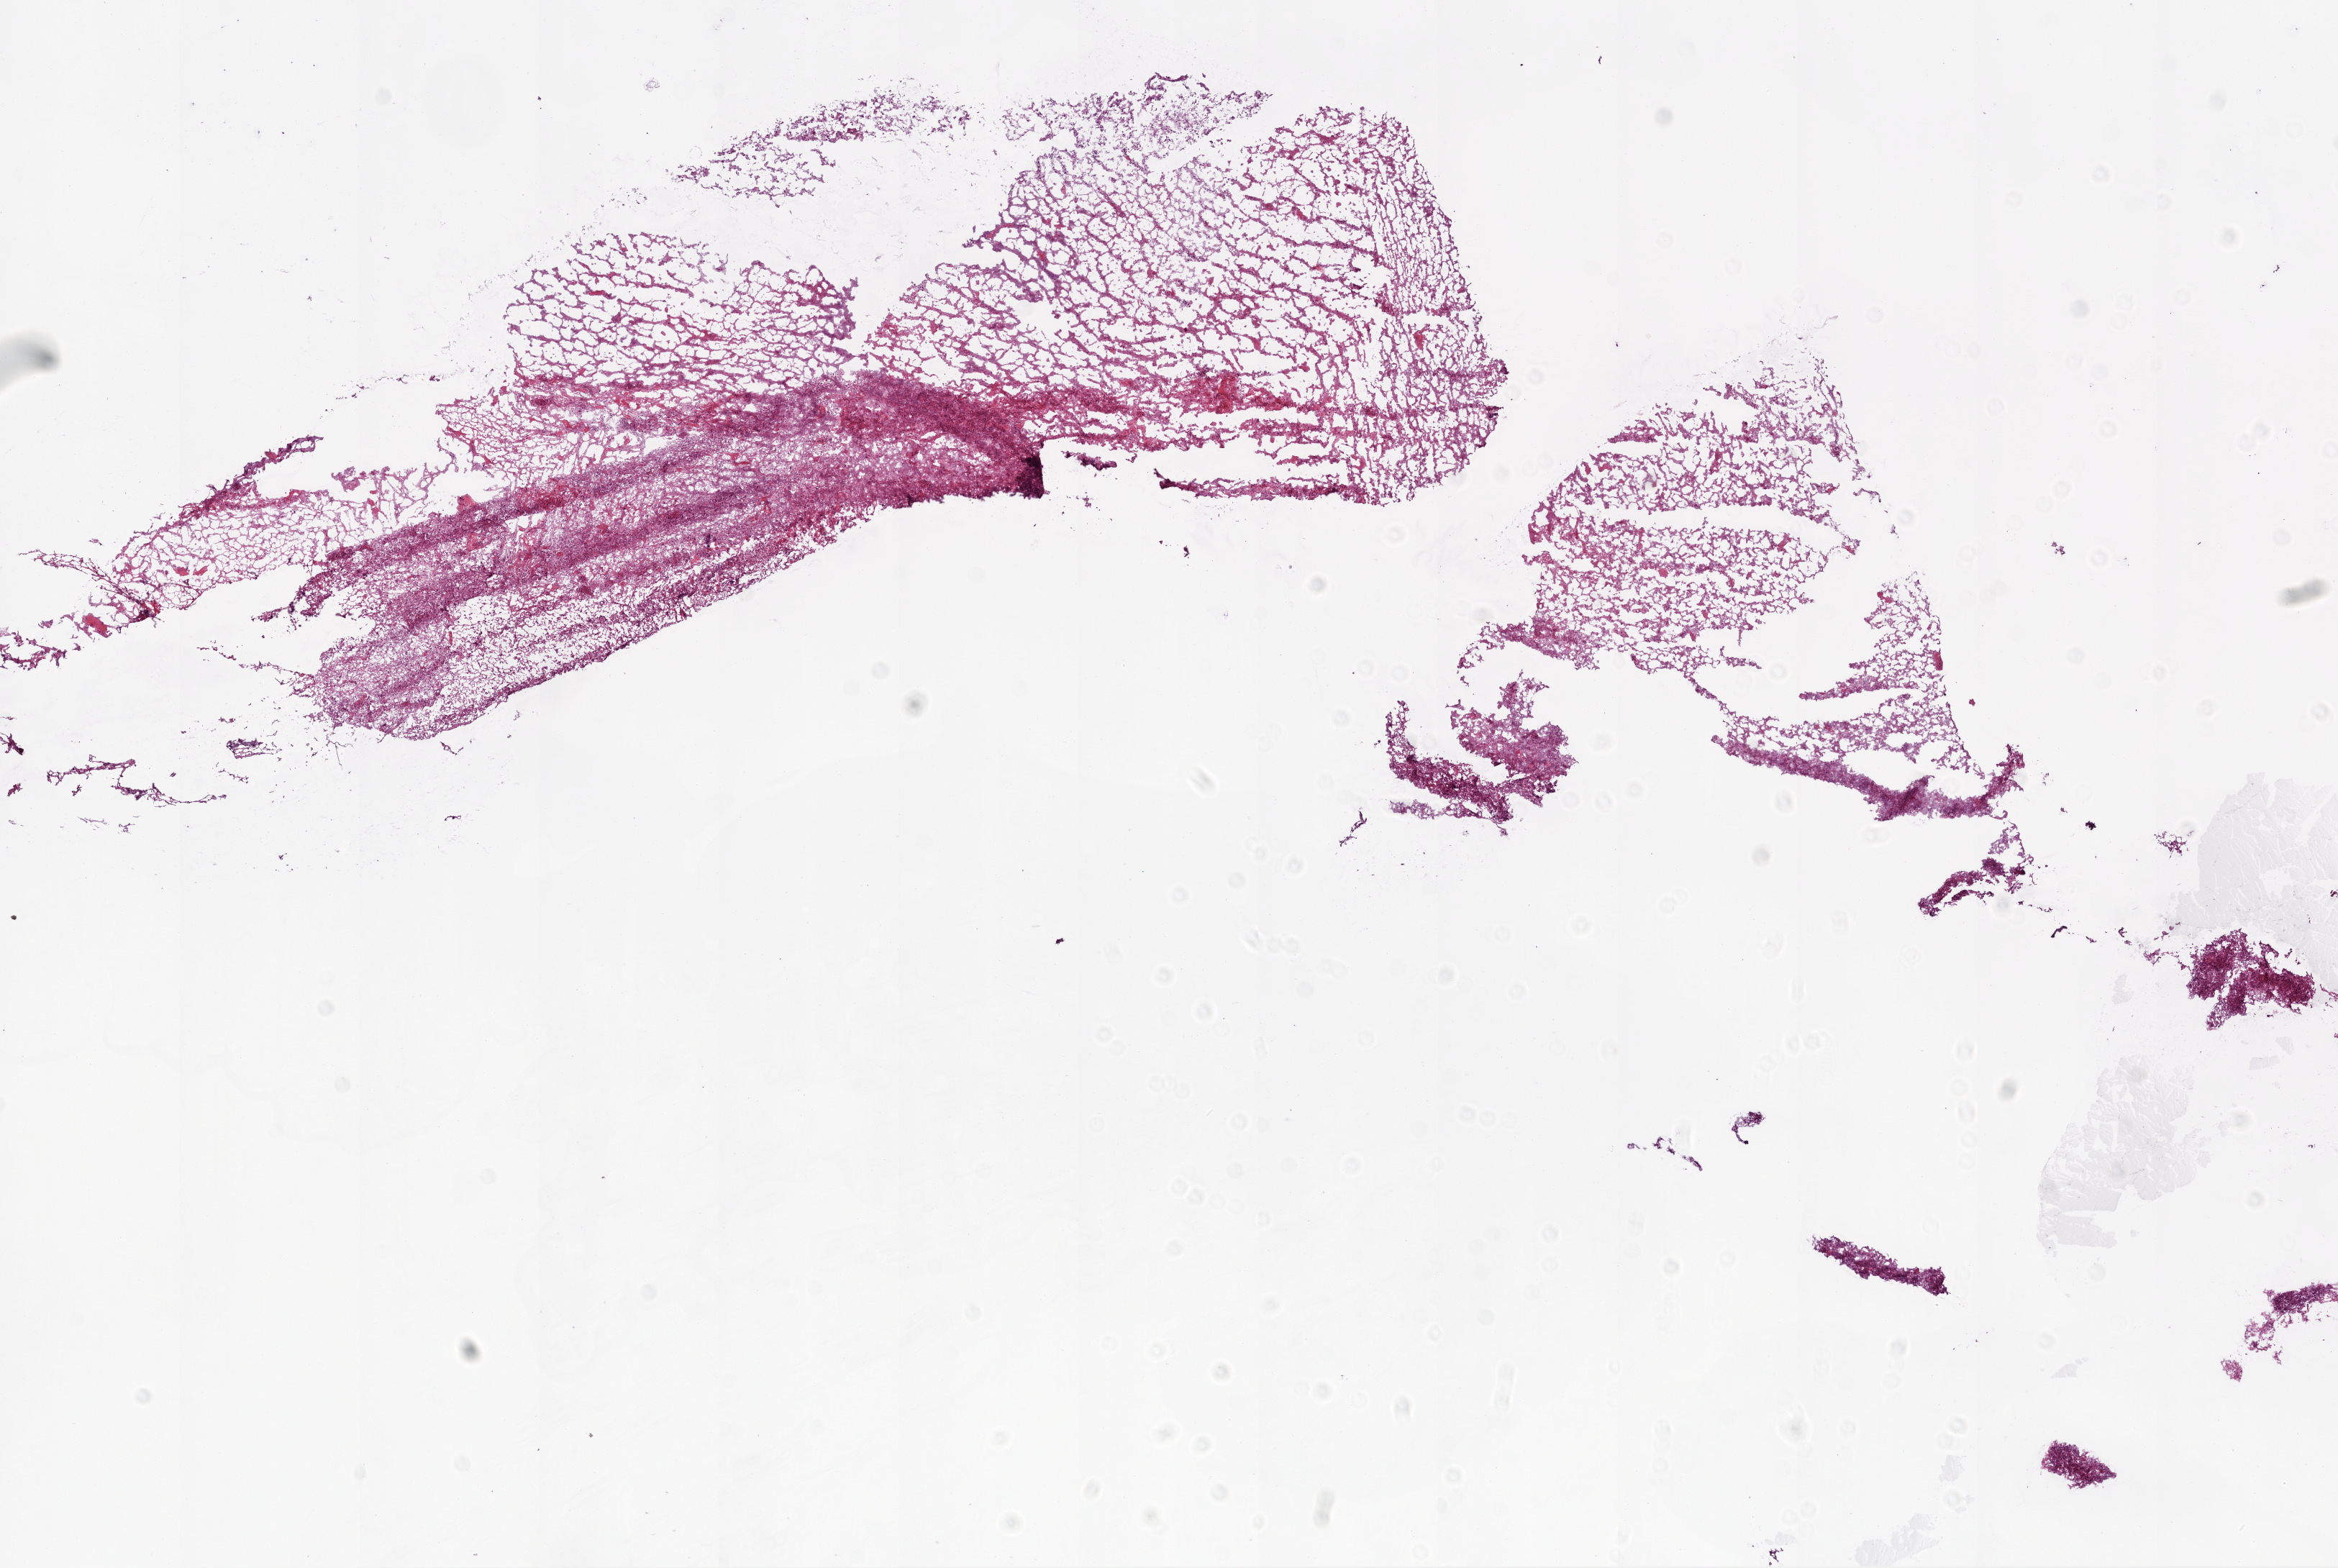
Whole-slide histology image, H&E — shown as a low-resolution overview of the whole scanned area (about 13.0 x 8.7 mm, from a 20x scan). Frozen section from the bottom of the tissue portion. Brain, primary tumour sample. Male patient; age at initial diagnosis 49 years. Composition of this section per pathologist review: tumour cells 90%, tumour nuclei 100%, normal cells 0%, stromal cells 0%, necrosis 10%.
• diagnosis: Glioblastoma